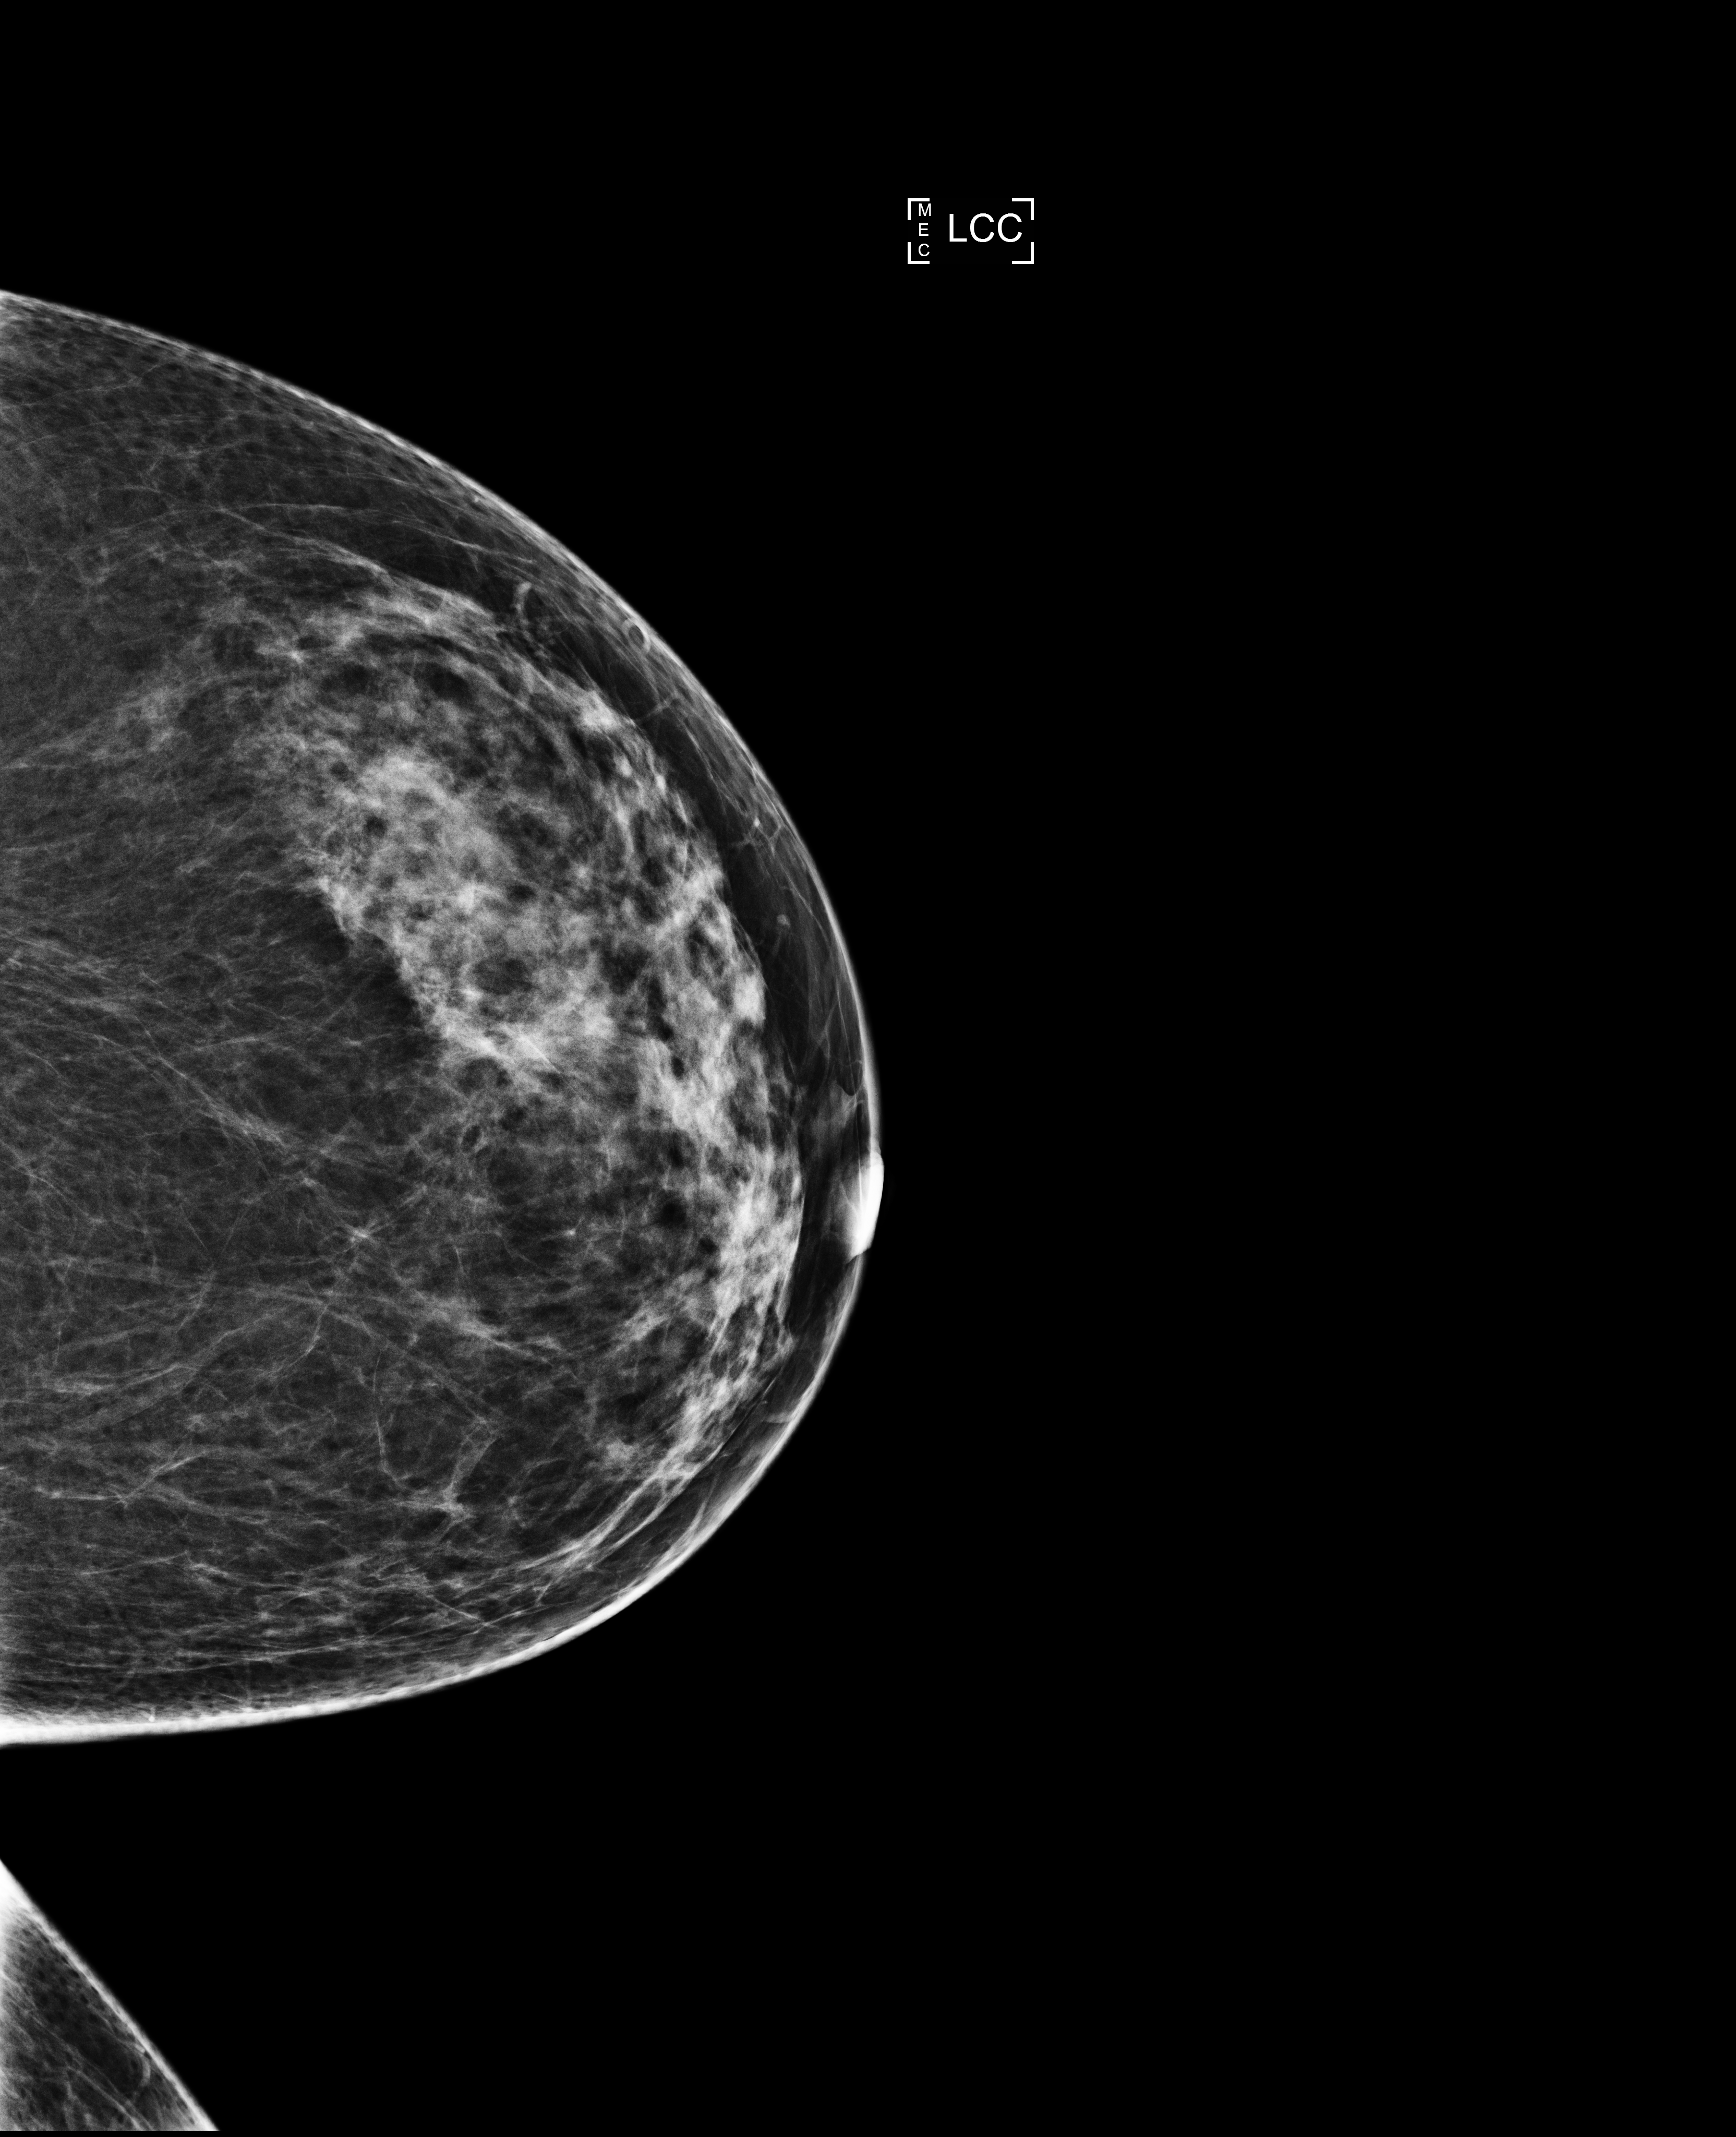
Full-field digital mammogram (FFDM), left breast, CC view, screening examination, compressed breast thickness 63 mm. Patient: female, 46 years.
BI-RADS breast density category at the screening exam (both breasts, scale 1–4): 3. Final BI-RADS category for the screening round (tomosynthesis exam, both breasts): category 1. Recall: no recall after this screen.